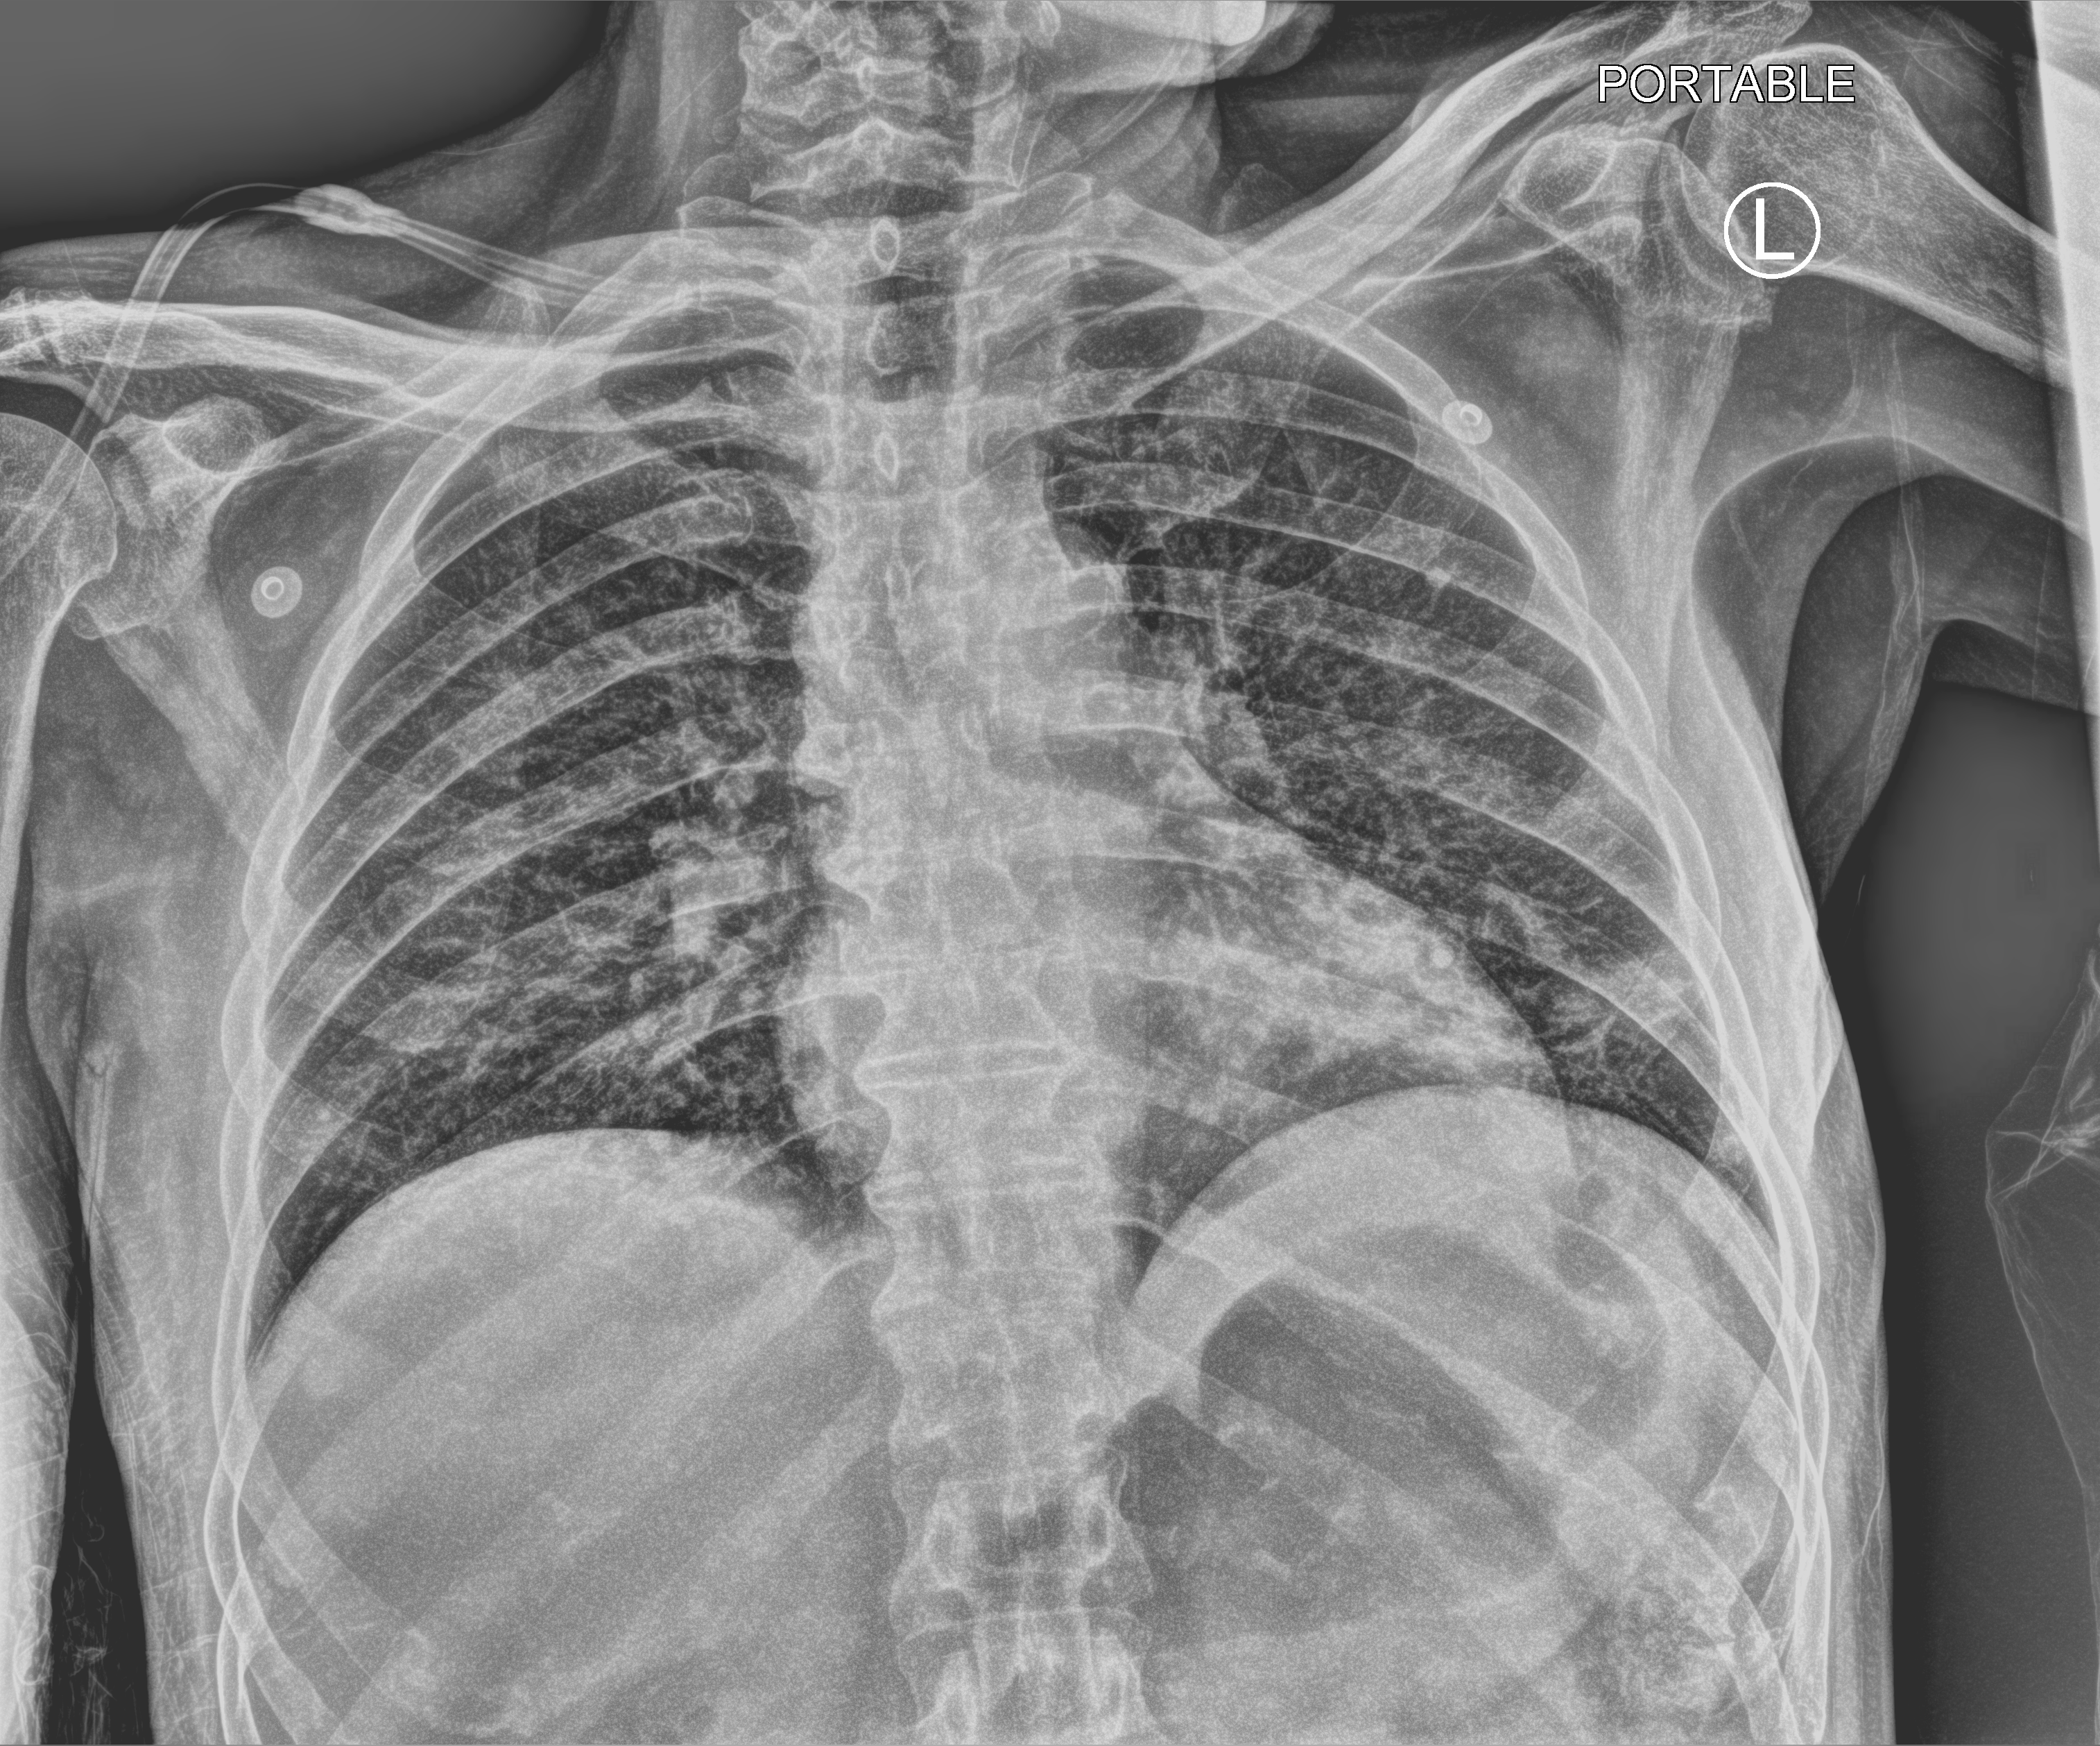
Chest X-ray (portable), anteroposterior (AP) projection. Patient hospitalised with COVID-19; male, aged 60–74 years.
Hospital-stay facts (about this admission, not read from this image; timing relative to this image not recorded): admitted to intensive care during this hospital stay: no.